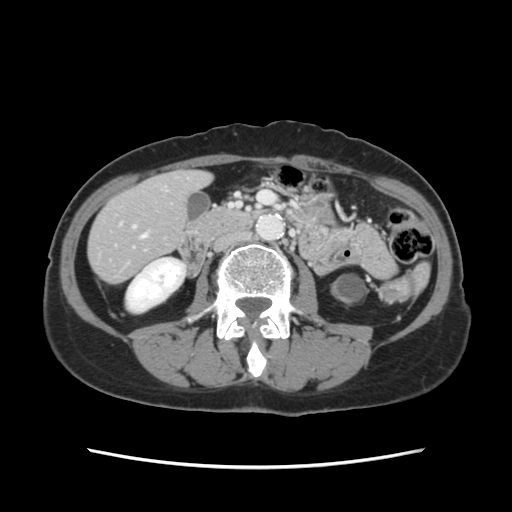
Contrast-enhanced abdominal CT, one axial slice; position 26 of 120 along the scan axis; 120 kVp; intravenous contrast given; soft-tissue window (W 400 / L 40 HU); 2.5 mm slice thickness; 512 × 512 image matrix, field of view 330 × 330 mm. Female patient, age 70 years. Case-level facts recorded for this patient, not image findings: diagnosis: colorectal cancer liver metastases, imaged before liver resection; multiple liver metastases: no; largest metastasis: 2.5 cm; chemotherapy before resection: yes.
Structures marked on this image (expert manual segmentation):
- hepatic veins: bounding box [x1, y1, x2, y2] px = [141, 234, 147, 238]
- liver: [90, 172, 208, 281]
- planned liver remnant (the part of the liver to remain after resection): [90, 172, 208, 281]
- portal vein (with intrahepatic branches): [132, 226, 136, 229]